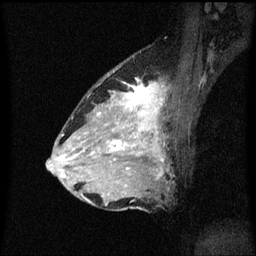
Breast MRI (dynamic contrast-enhanced), one sagittal slice. Slice 36 of 60 in the series (ordered by position). Dynamic contrast-enhanced series, image 2 of 3 at this slice position (ordered by acquisition). 1.5 T. TE 4.2 ms, TR 8.4 ms. 2 mm slice thickness. 256 × 256 image matrix, field of view 200 × 200 mm. Female patient, age 34 years. From the clinical record (not read from this slice): setting: breast cancer imaged before/during neoadjuvant chemotherapy; receptor status: HR-positive, HER2-negative.
Outlined on this slice (semi-automatically segmented with operator editing):
- analysis volume of interest (the breast-tissue region the enhancement analysis was run in; not a lesion): bounding box <69,70,175,209> (left, top, right, bottom; pixels)
- tumour enhancement mask (voxels above the 70 % enhancement threshold inside the analysis volume of interest): <81,82,164,197>